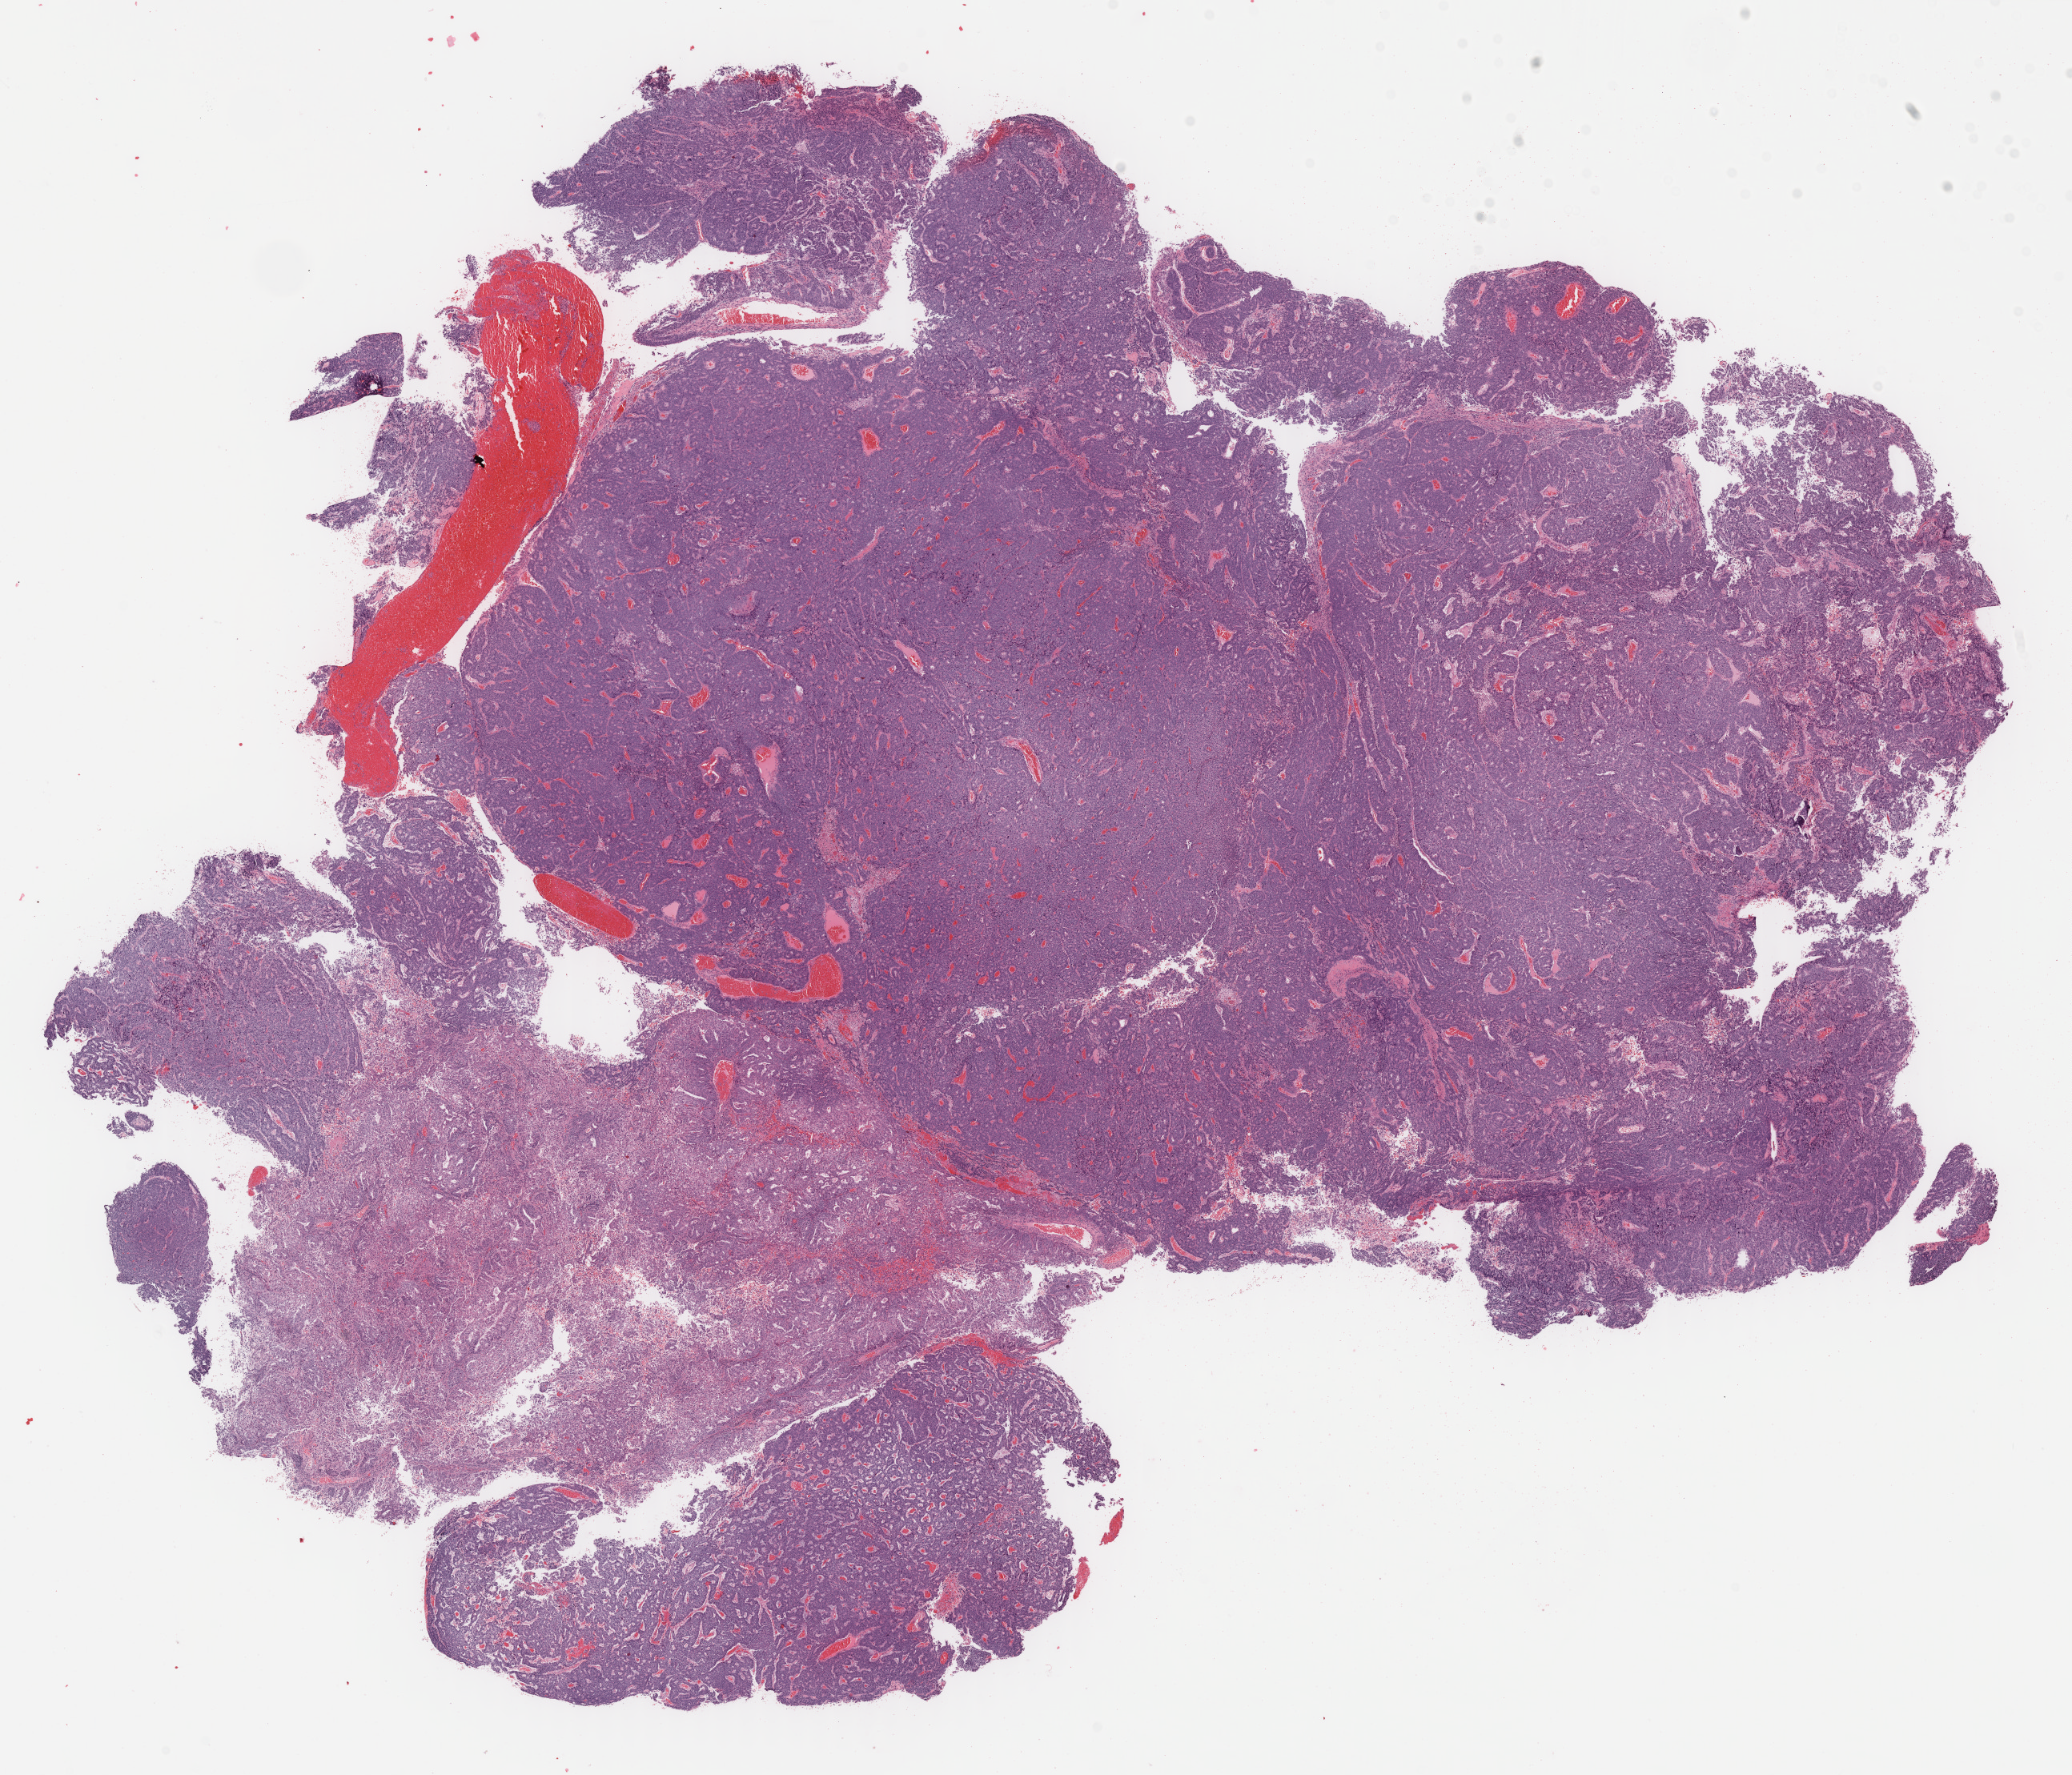
Digitized H&E-stained tissue section (whole slide) — low-resolution overview of the scanned area, about 20.5 x 17.5 mm (slide scanned at 40x). Formalin-fixed paraffin-embedded (FFPE) diagnostic section. Uterus, primary tumour sample. Female patient; age at initial diagnosis 75 years. Histologic grade: G3 (poorly differentiated).
FIGO stage: IA. Pathologic diagnosis: Endometrioid adenocarcinoma, NOS (endometrium).